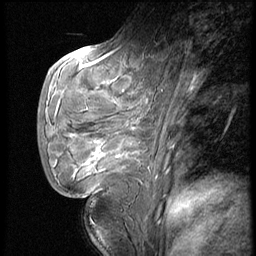
Breast MRI (dynamic contrast-enhanced), one sagittal slice; slice 21 of 62 in the series (ordered by position); dynamic contrast-enhanced series, image 2 of 4 at this slice position (ordered by acquisition); 1.5 T; TE 4.2 ms, TR 9 ms; 2.5 mm slice thickness; 256 × 256 image matrix, field of view 180 × 180 mm. Patient: female, 28 years. Case-level facts recorded for this patient, not image findings: setting: breast cancer imaged before/during neoadjuvant chemotherapy.
Annotated regions visible in this slice (semi-automatic segmentation, software-assisted and operator-edited):
- analysis volume of interest (the breast-tissue region the enhancement analysis was run in; not a lesion): bounding box <44,54,150,183> (left, top, right, bottom; pixels)
- tumour enhancement mask (voxels above the 140 % enhancement threshold inside the analysis volume of interest): <74,144,139,177>